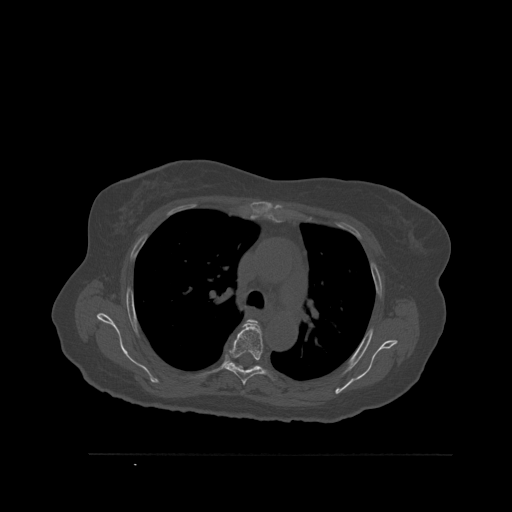
CT including the spine, one axial slice; position 394 of 527 along the scan axis; bone window (W 1800 / L 400 HU); 1.5 mm slice thickness; 512 × 512 image matrix, field of view 470 × 470 mm. Patient: female, 73 years. From the clinical record (not read from this slice): primary cancer: breast; vertebrae with lytic lesions (as recorded): L2.
Annotated regions visible in this slice (semi-automatically segmented with operator editing):
- T4 vertebra: bounding box <246,319,258,325> (left, top, right, bottom; pixels)
- T5 vertebra: <224,324,267,385>
- T6 vertebra: <229,362,262,370>